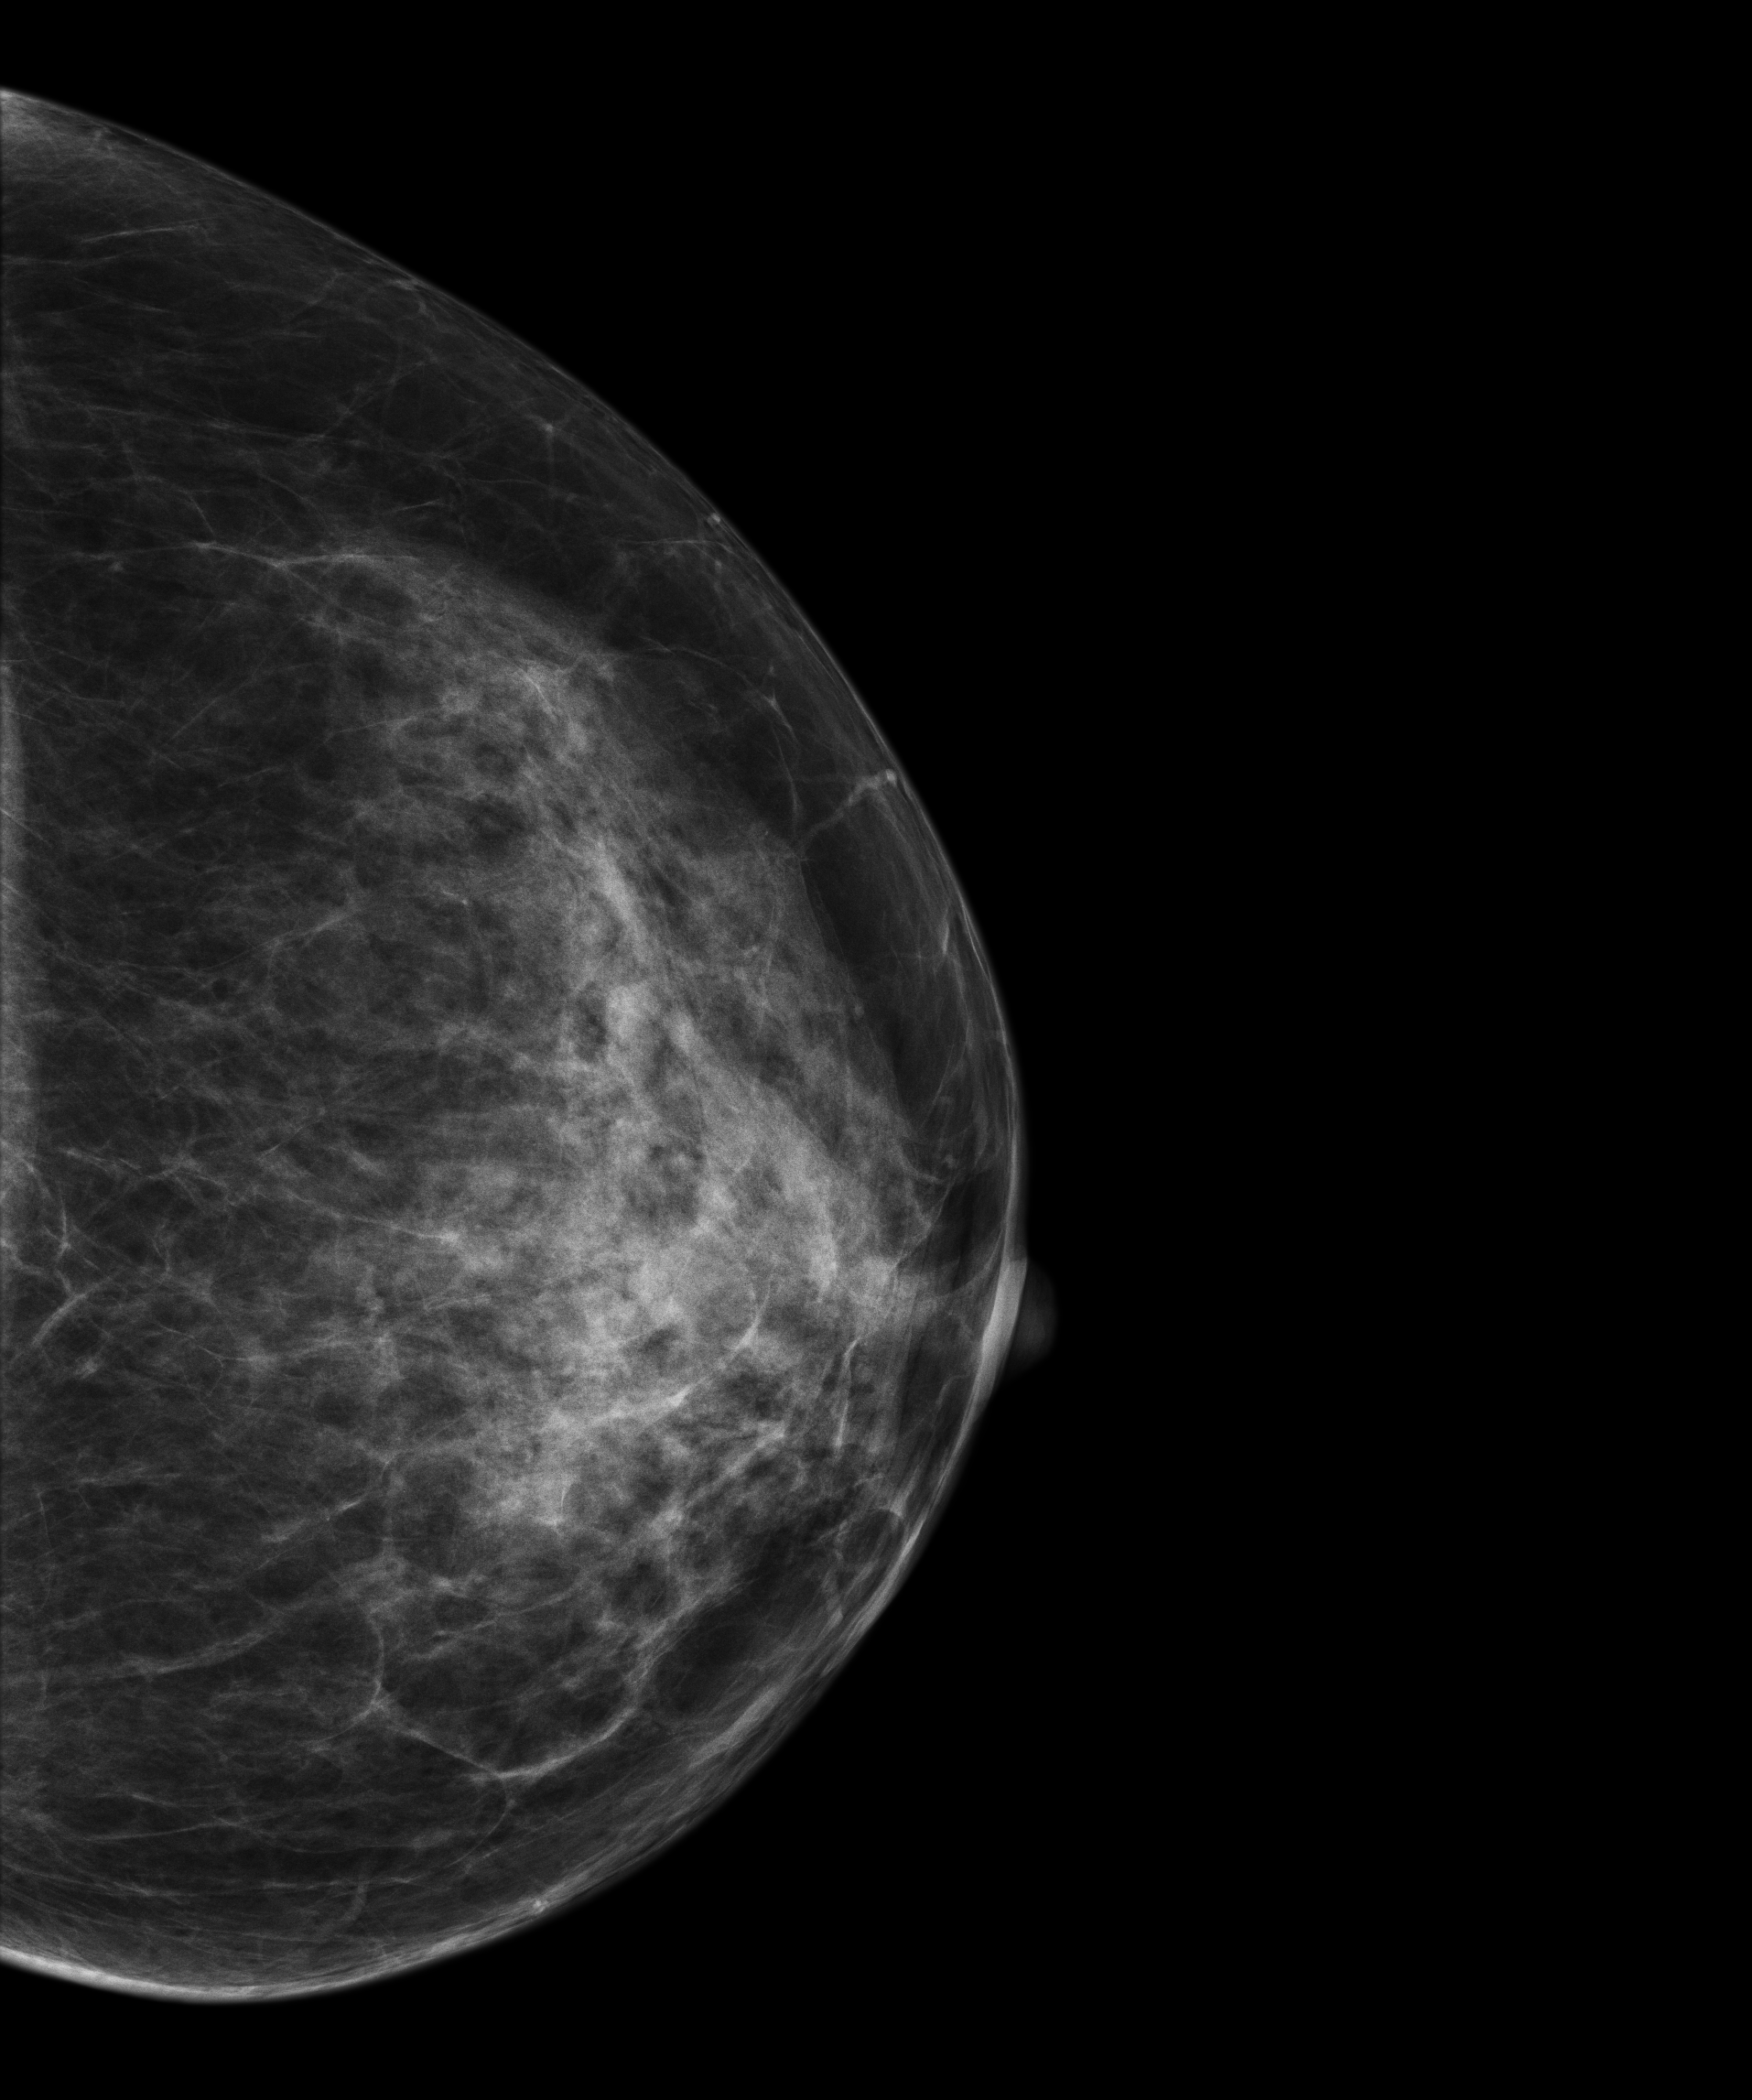
Full-field digital mammogram (FFDM); left breast; craniocaudal (CC) view; screening examination; compressed breast thickness 43 mm. Patient: female, 53 years.
Breast density at the screening exam (both breasts): heterogeneously dense (BI-RADS density category c). Final BI-RADS category for the screening round (tomosynthesis exam, both breasts): category 1. Recall: no recall after this screen.